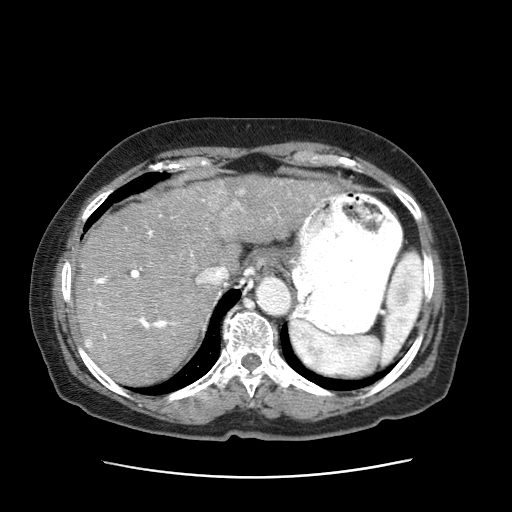
Contrast-enhanced abdominal CT (liver protocol), one axial slice; position 53 of 63 along the scan axis; 120 kVp; intravenous contrast given; soft-tissue window (W 400 / L 40 HU); 512 × 512 image matrix, field of view 360 × 360 mm. Patient: female, 79 years. From the clinical record (not read from this slice): diagnosis: hepatocellular carcinoma (patient treated with transarterial chemoembolisation; whether this scan precedes or follows treatment is not stated here); TNM stage (as recorded): Stage-II.
Structures marked on this image (semi-automatic segmentation, software-assisted and operator-edited):
- abdominal aorta: bounding box <256,278,292,316> (left, top, right, bottom; pixels)
- liver parenchyma outside the tumour (the mass and vessels are separate outlines, so this box may not span the whole liver): <78,181,245,388>
- mass: <208,176,337,245>
- liver vessels: <94,201,245,340>